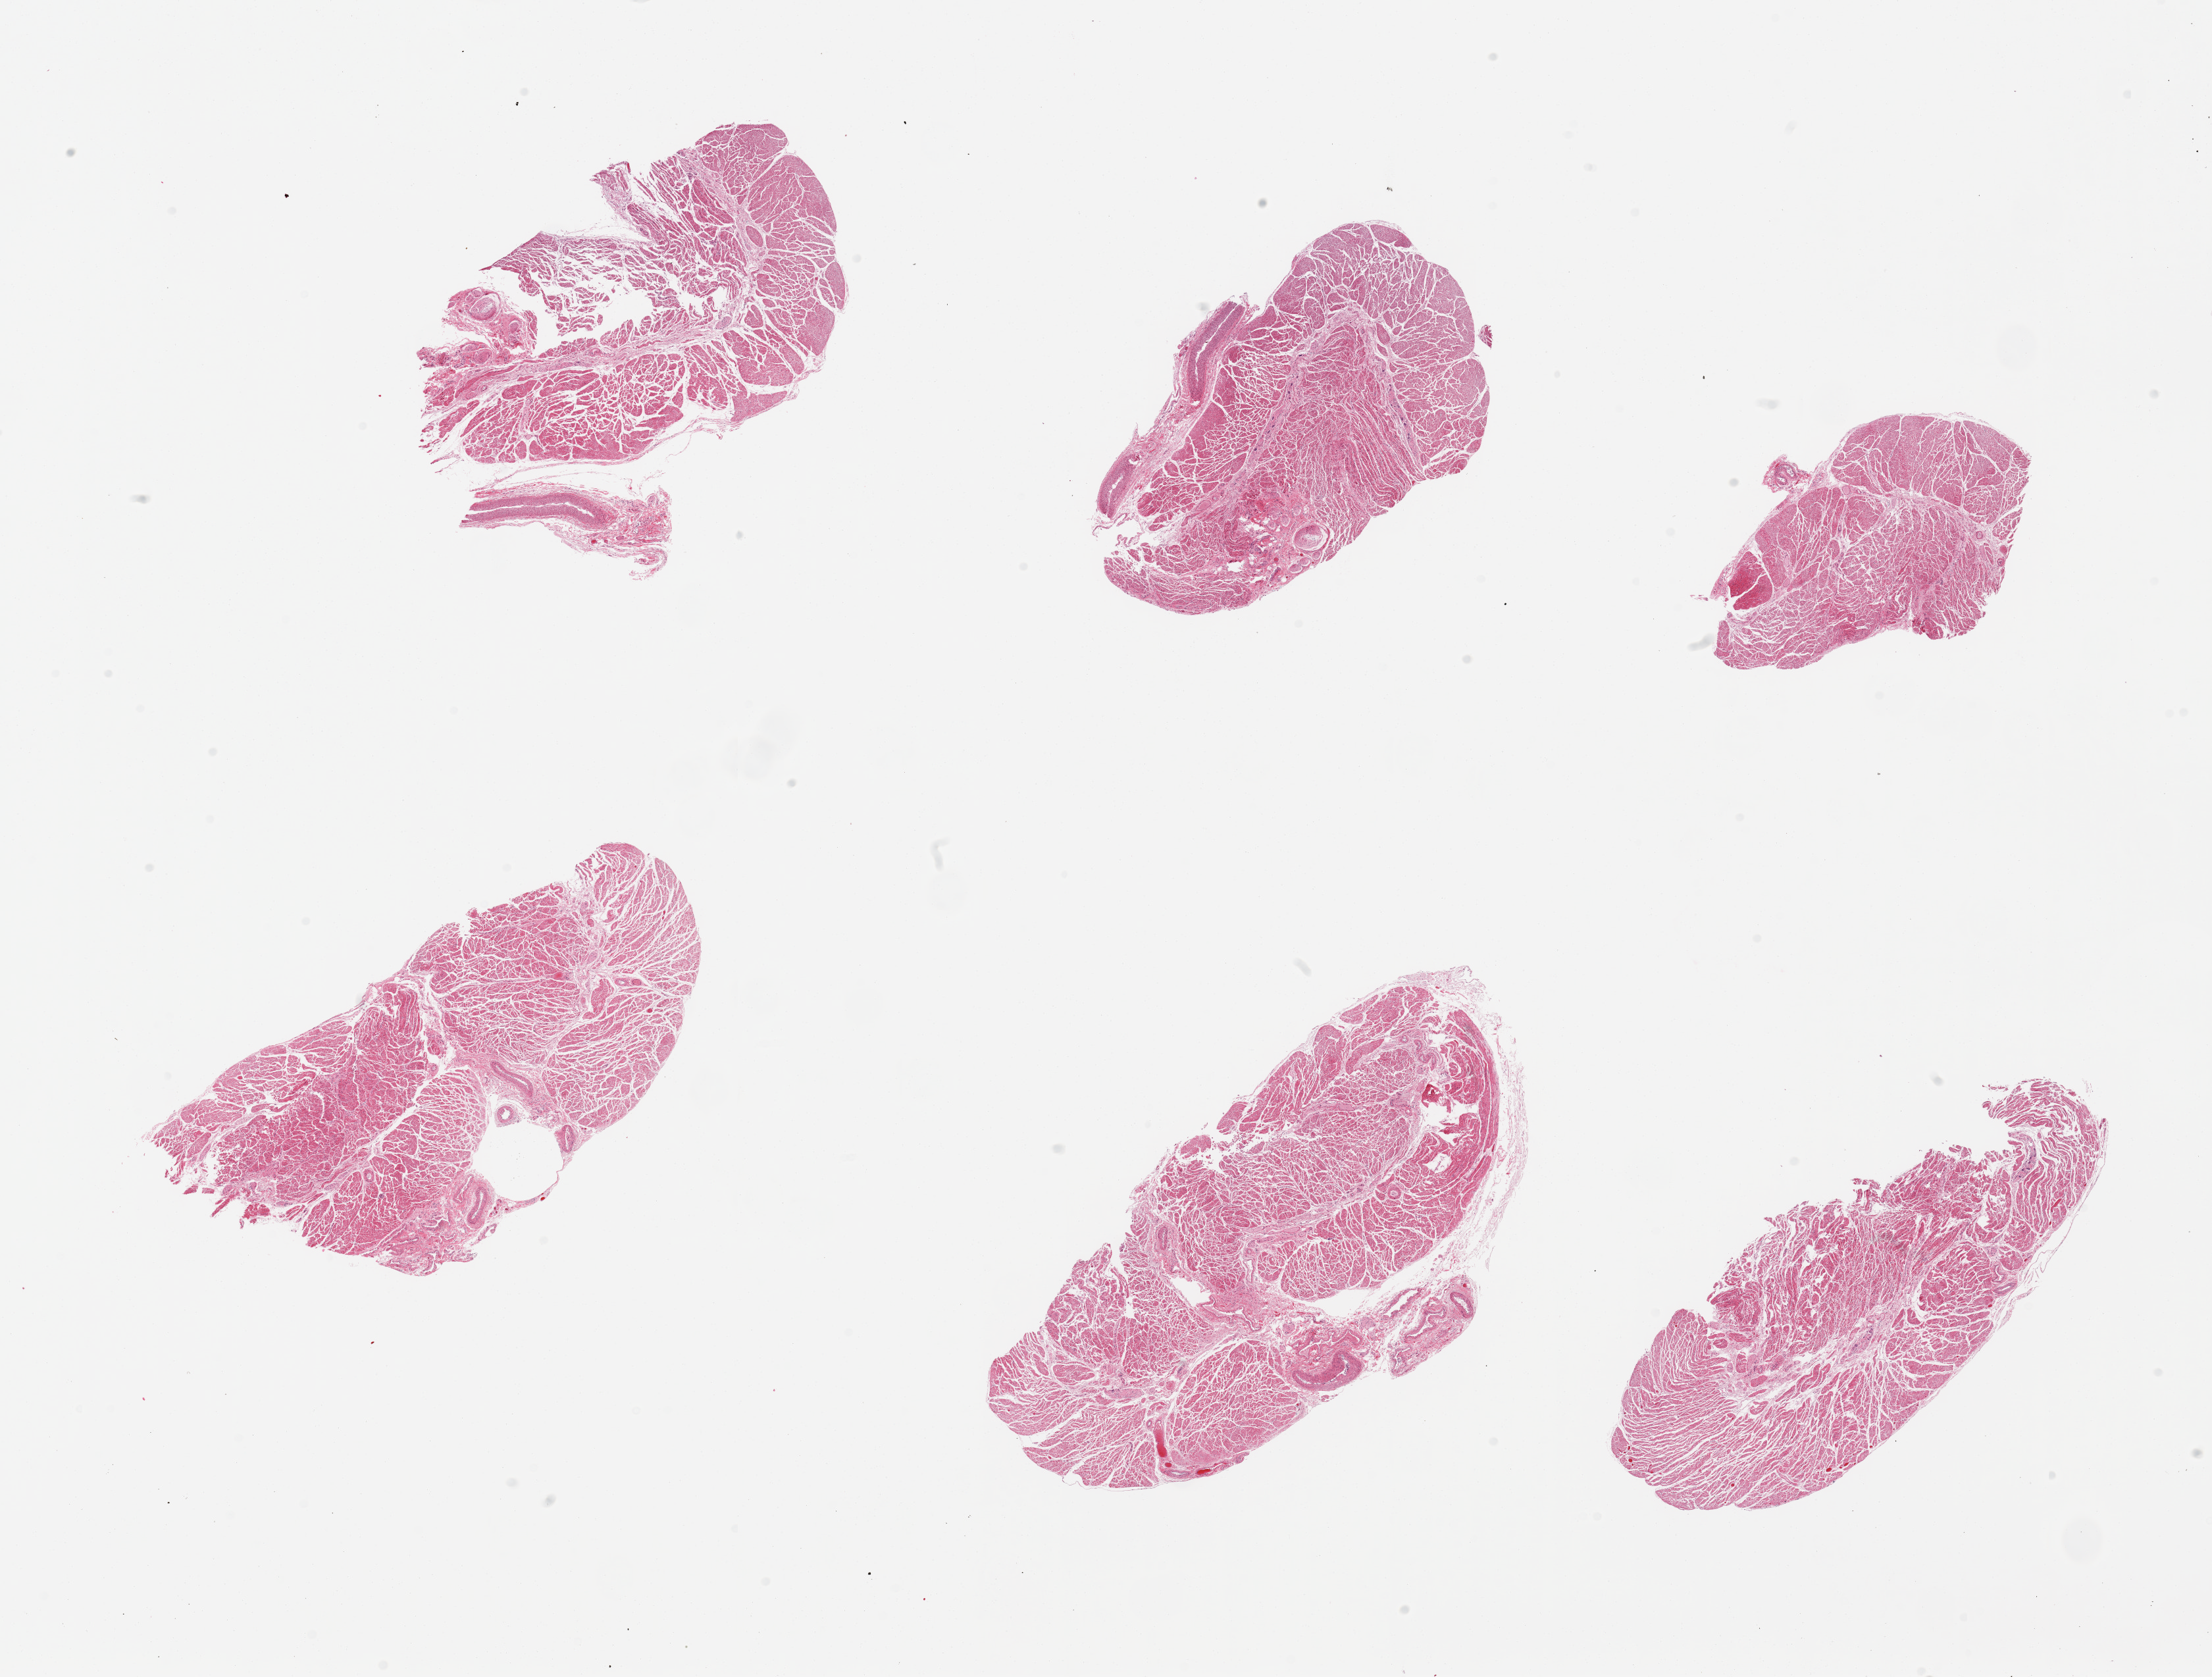
Digitized haematoxylin and eosin-stained section — low-resolution overview of the scanned area, about 26.6 x 20.2 mm, PAXgene-fixed, paraffin-embedded tissue, target tissue: esophageal muscle, tissue donor sample. Female donor.
Review note (as recorded): 6 pieces.